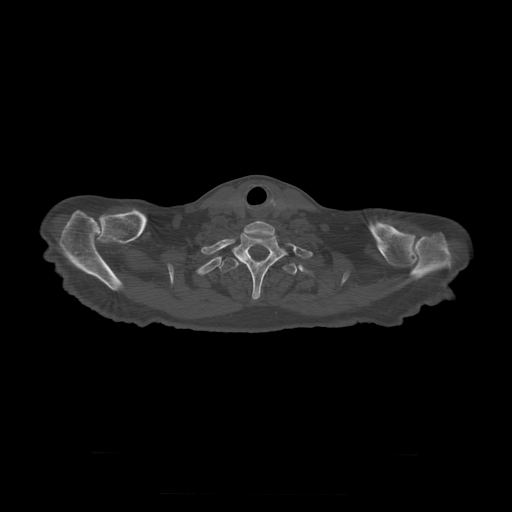
CT including the spine, one axial slice; position 286 of 397 along the scan axis; reconstruction kernel STANDARD; 120 kVp; bone window (W 1800 / L 400 HU); 1.25 mm slice thickness; 512 × 512 image matrix, field of view 510 × 510 mm. Patient age 73 years. From the clinical record (not read from this slice): primary cancer: prostate.
Annotated regions visible in this slice (semi-automatically segmented with operator editing):
- T1 vertebra: bounding box [x1, y1, x2, y2] px = [234, 231, 286, 300]
- T2 vertebra: [220, 258, 298, 276]